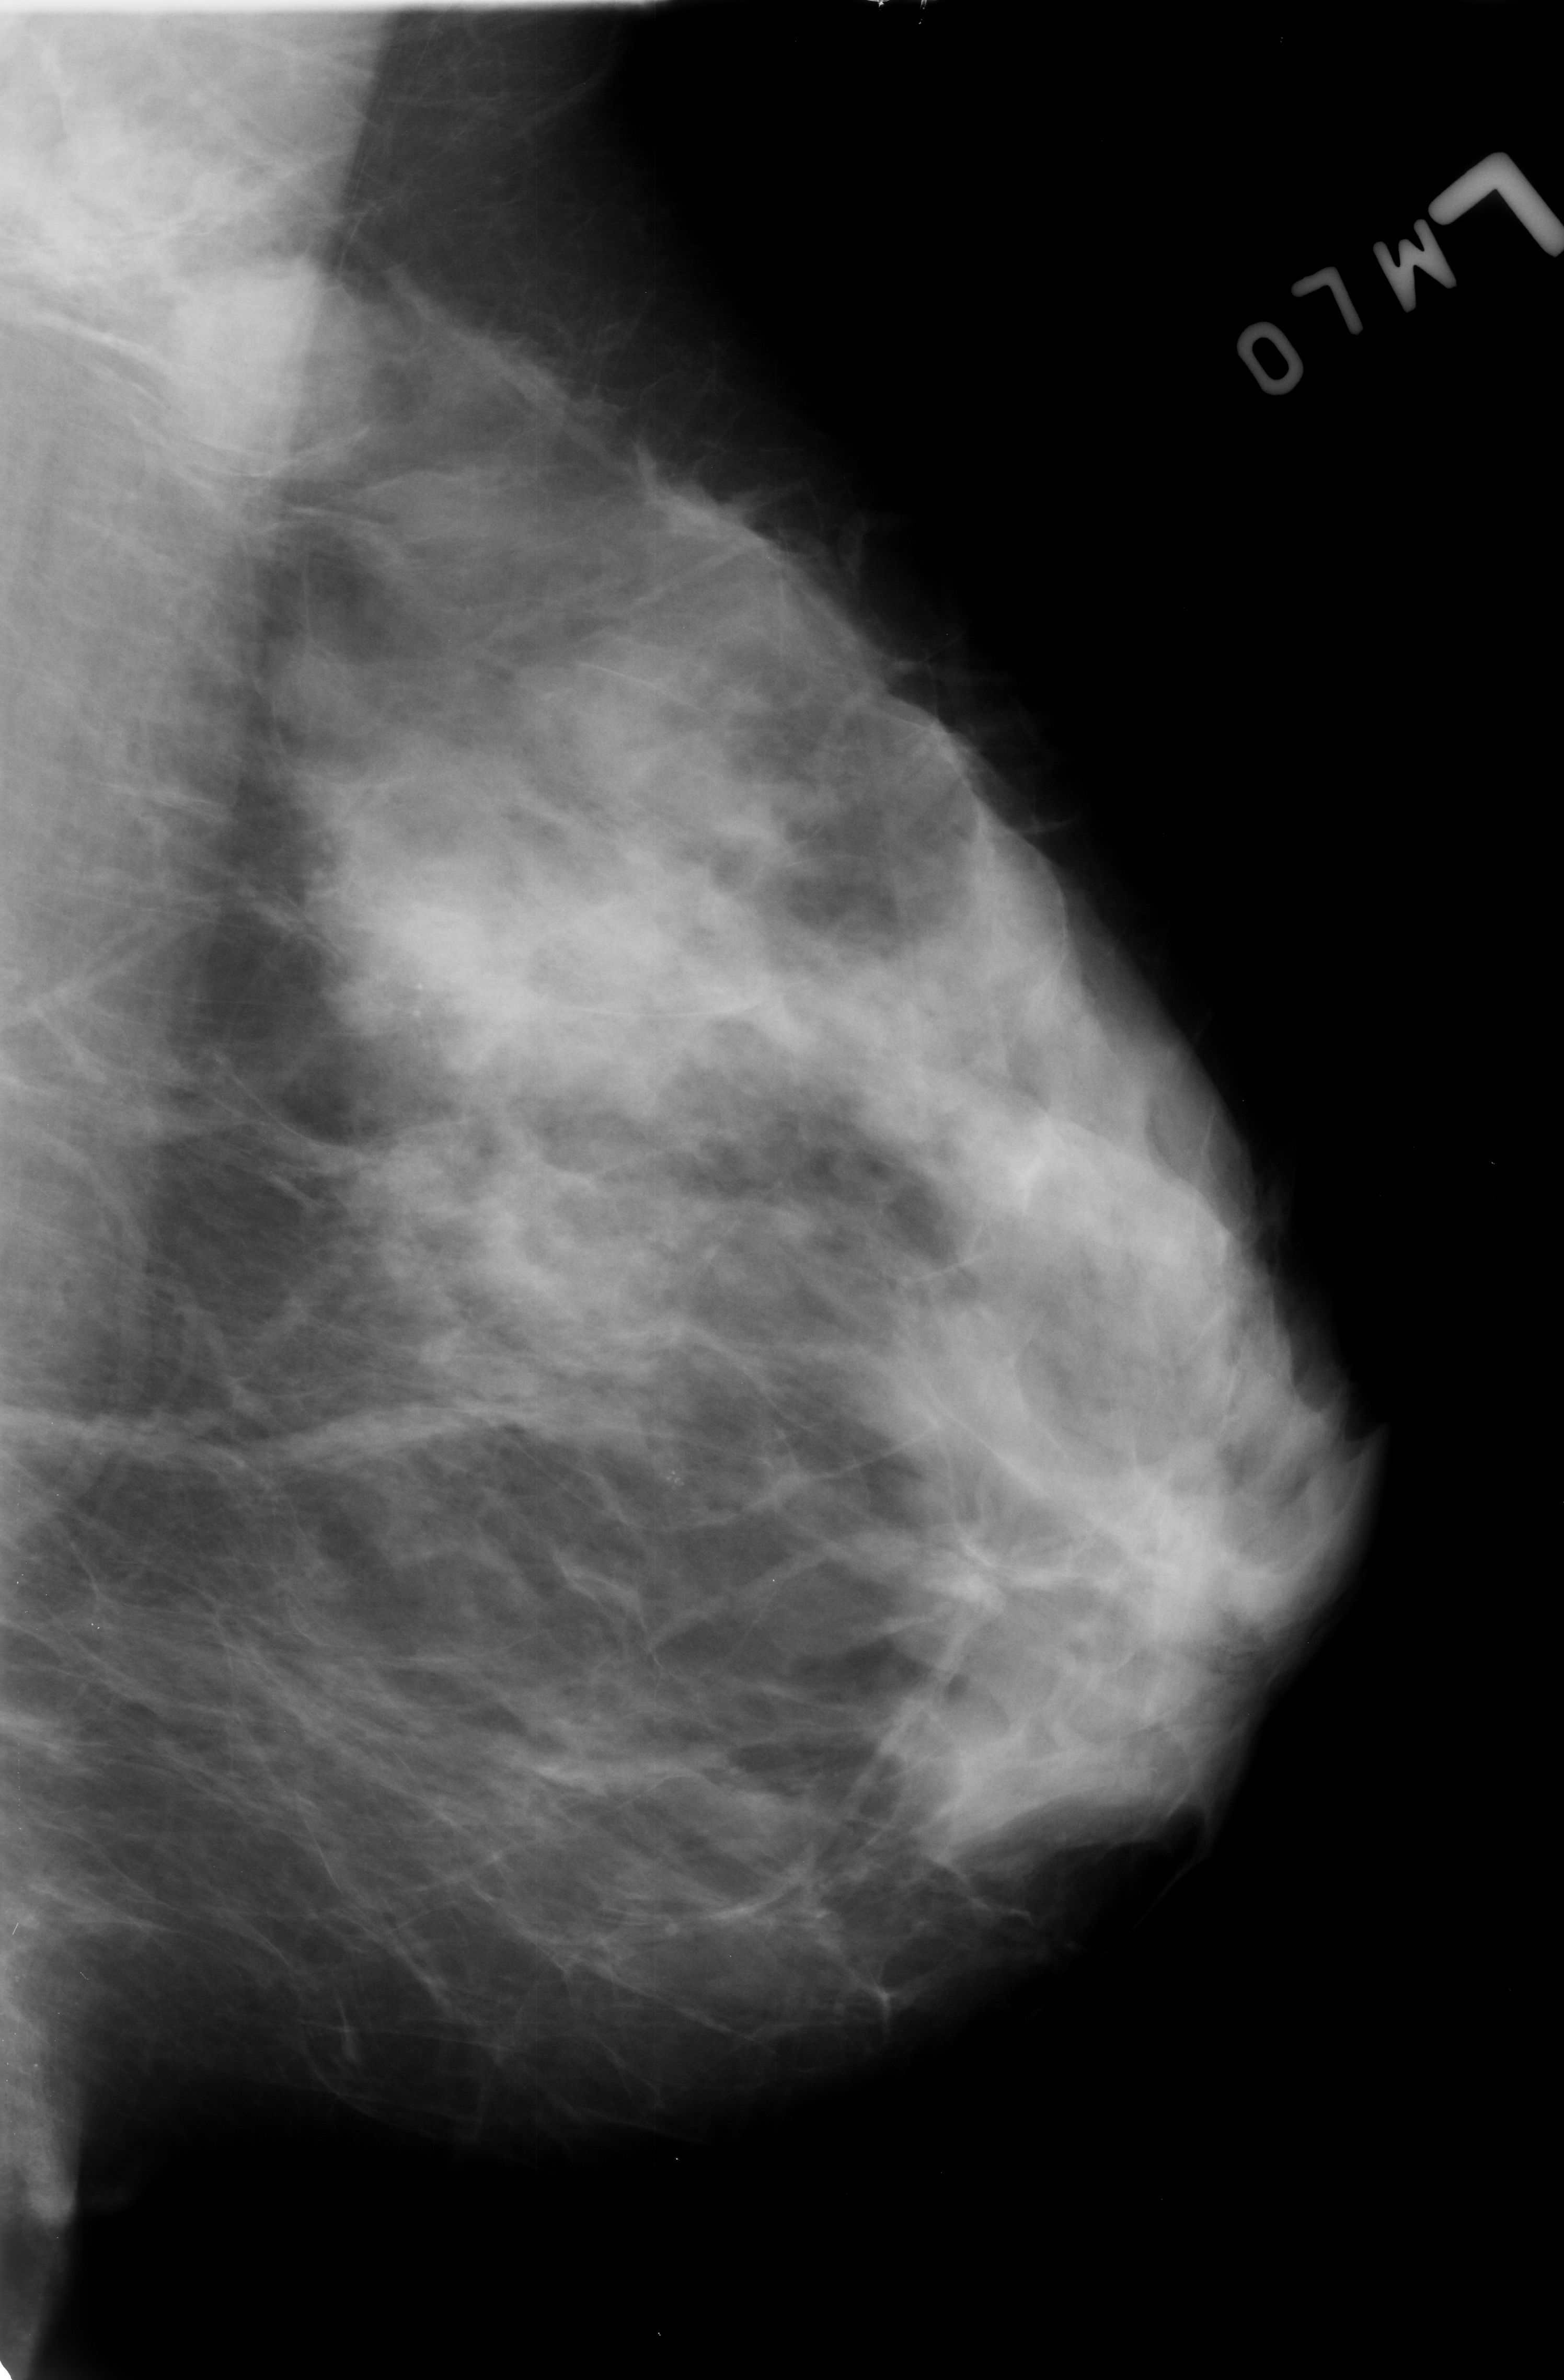
Scanned film-screen mammogram, left breast, mediolateral oblique (MLO) view, breast composition: heterogeneously dense (BI-RADS density category 3 of 4).
Radiologist-marked abnormalities on this image: calcifications, morphology pleomorphic, distribution clustered; BI-RADS assessment category 4; subtlety rating 3 on a 1 (subtle) to 5 (obvious) scale; pathology result (as recorded, not read from the image): benign.